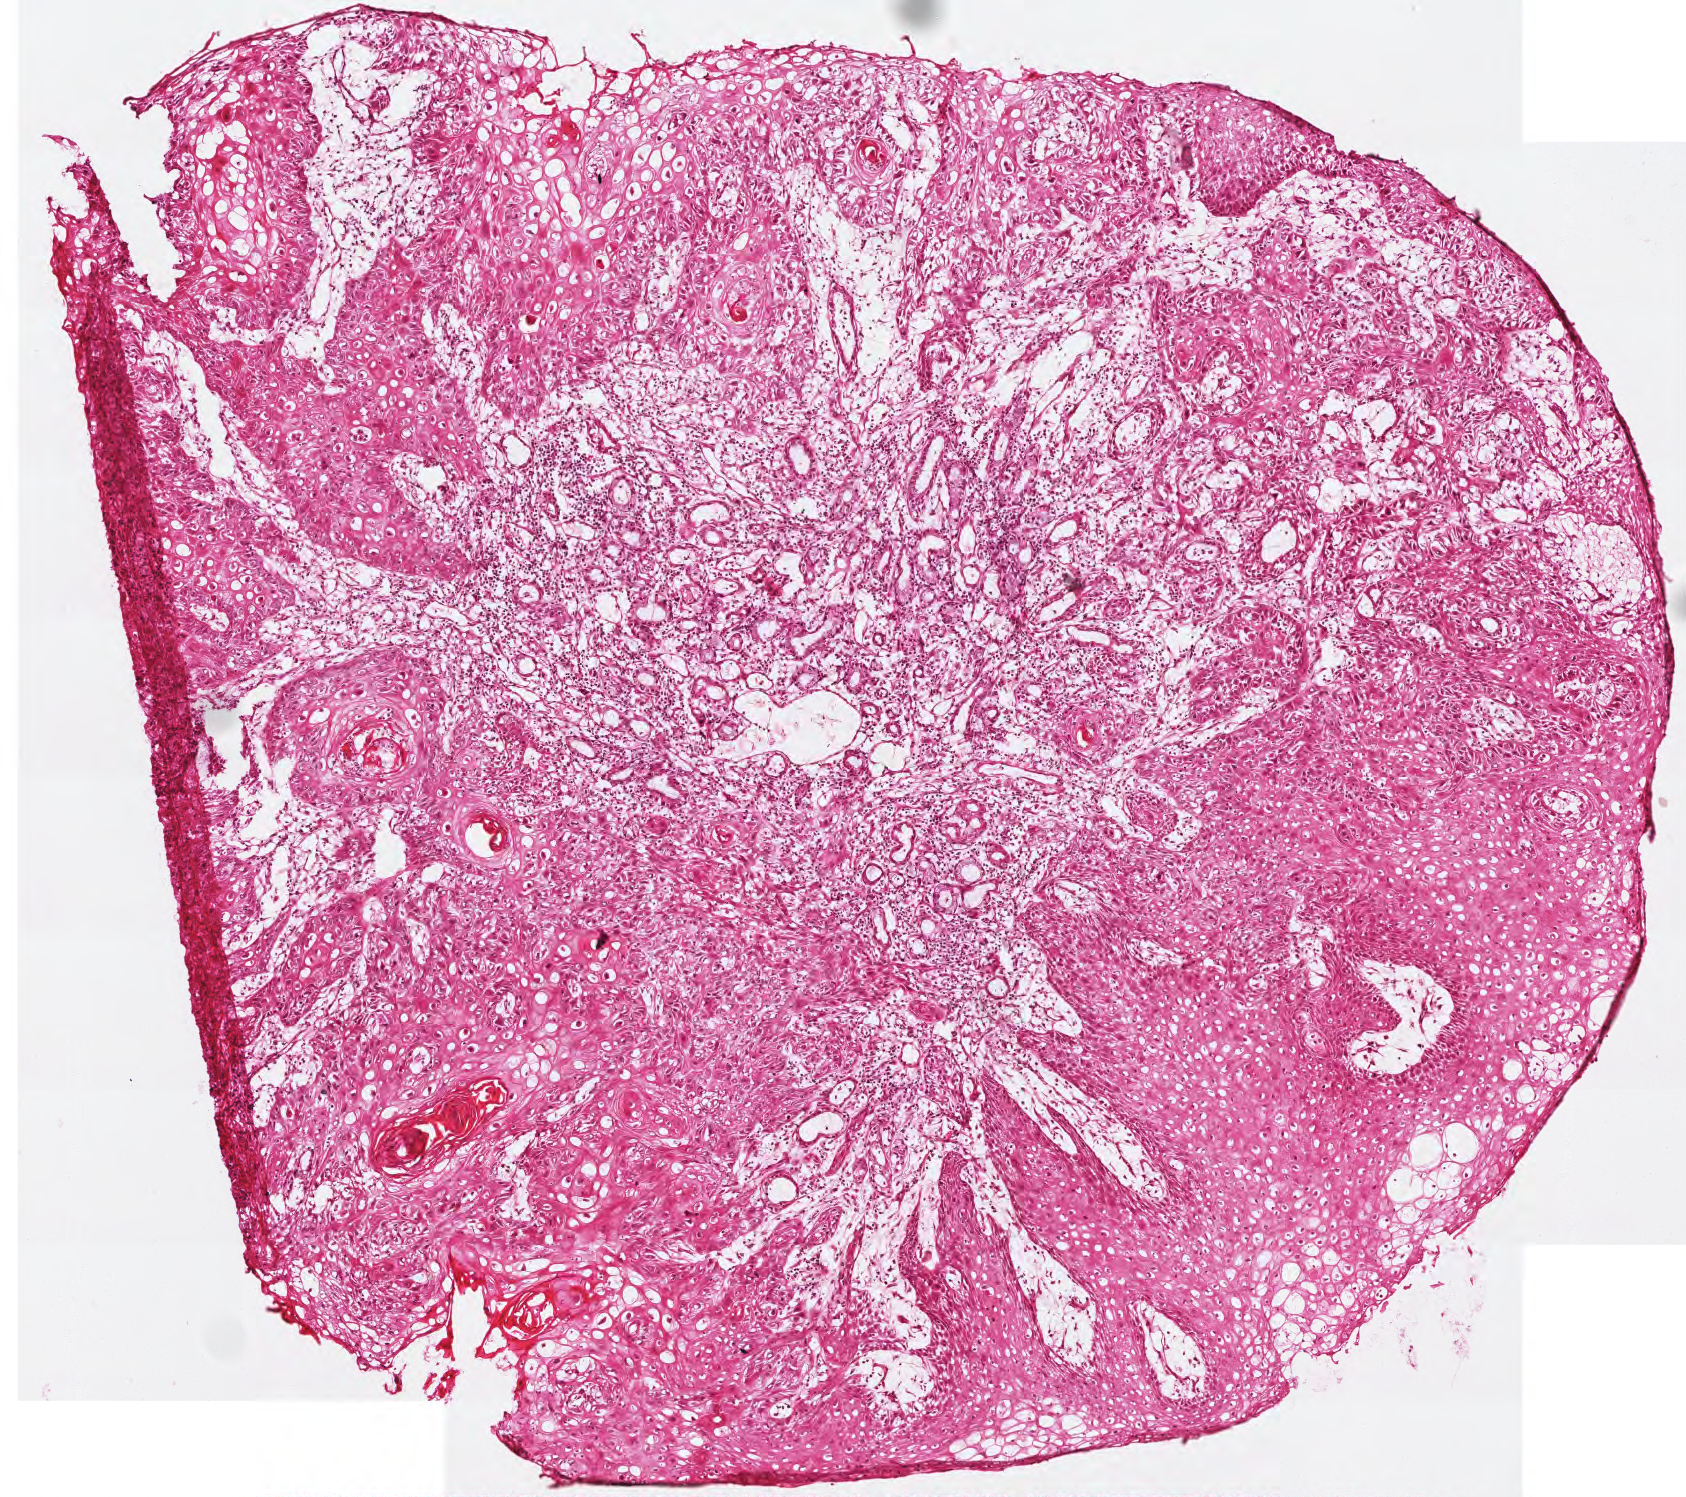
Whole-slide histology image, H&E, a low-resolution overview of the entire scanned area, about 3.4 x 3.0 mm. Frozen section from the top of the tissue portion. Primary tumour sample from the head and neck. Patient: male, age at initial diagnosis 78 years. Histologic grade: G3 (poorly differentiated). Composition of this section per pathologist review: tumour cells 65%, tumour nuclei 75%, normal cells 15%, stromal cells 20%, necrosis 0%.
AJCC pathologic stage: III (7th edition). Diagnosis: Squamous cell carcinoma, NOS (hard palate). Laterality: right.